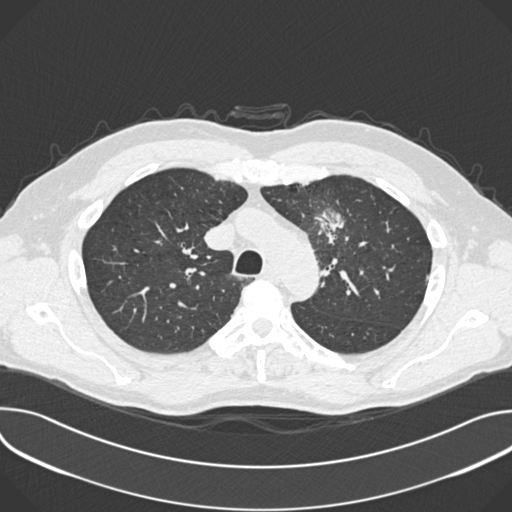
Low-dose screening chest CT, one axial slice. Position 272 of 361 along the scan axis. Lung window (W 1500 / L -600 HU). 1 mm slice thickness. 512 × 512 image matrix.
Outlined on this slice (manually delineated by an expert):
- lesion 1 (tumor, upper lobe of left lung): box from (x=319, y=212) to (x=343, y=240) px